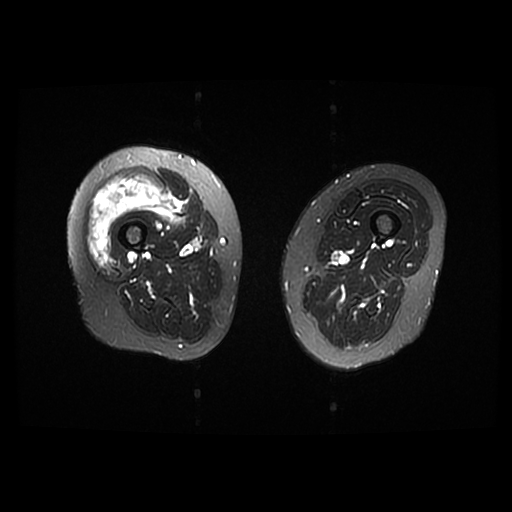
MRI of an extremity soft-tissue mass, one axial slice; slice 12 of 42 in the series (ordered by position); T2-weighted fat-saturated; 6 mm slice thickness; 512 × 512 image matrix. Female patient. Case-level facts recorded for this patient, not image findings: histological type: pleiomorphic undifferentiated sarcoma; grade: high; site of the primary tumour: right quadricep.
Annotated regions visible in this slice (expert manual segmentation):
- gross tumour volume including surrounding oedema: bounding box <87,175,181,266> (left, top, right, bottom; pixels)
- gross tumour volume (mass): <87,175,181,266>